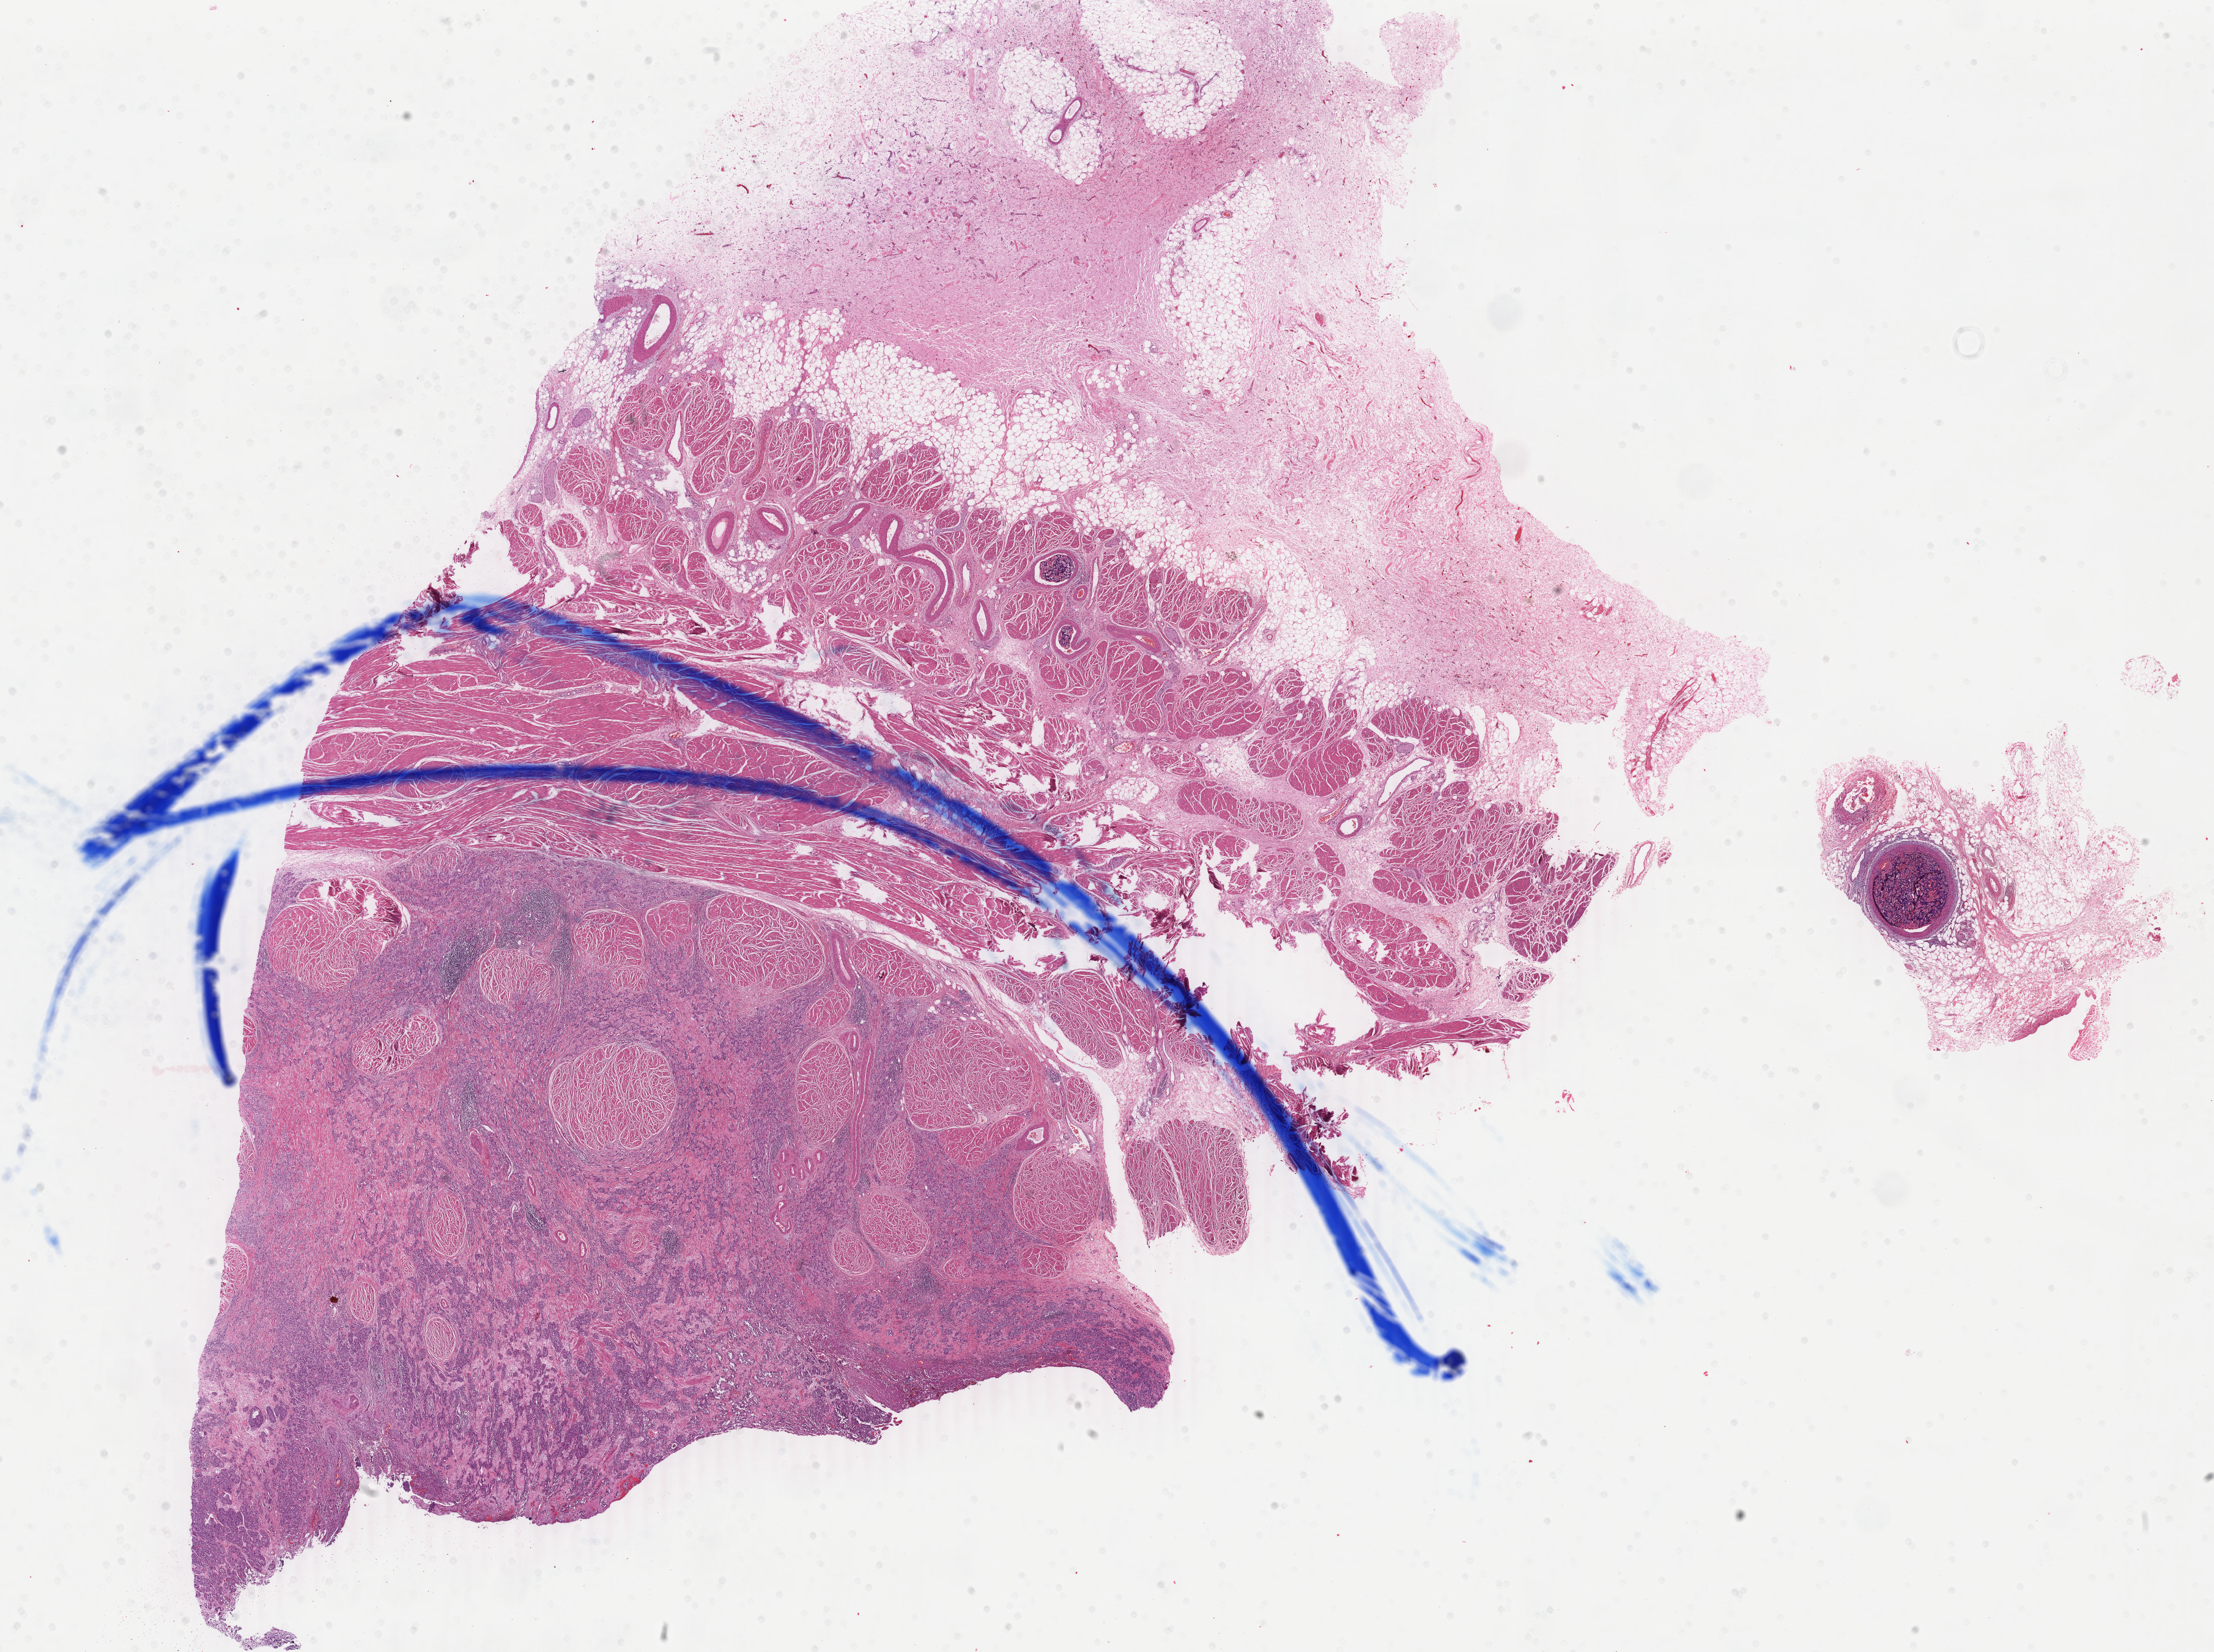
Digitized H&E tissue section (whole slide) — shown as a low-resolution overview of the whole scanned area (about 28.8 x 21.5 mm). FFPE section. Sample: primary tumour, bladder. Patient: female, age at initial diagnosis 47 years. Histologic grade: high grade.
- histologic diagnosis: Transitional cell carcinoma (lateral wall of bladder)
- AJCC pathologic stage: II (7th edition)